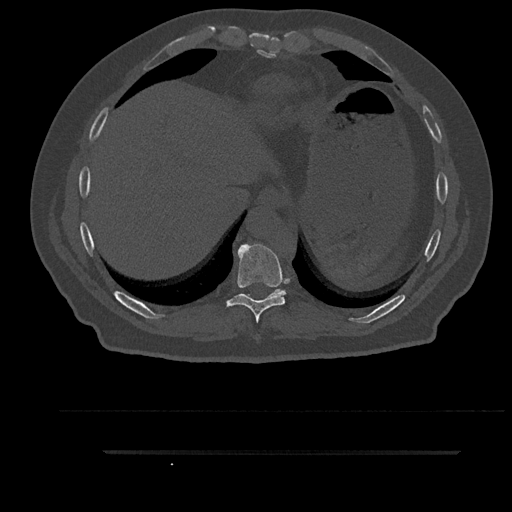
CT including the spine, one axial slice; slice 419 of 797 in the series (ordered by position); reconstruction kernel Br40s/3; 120 kVp; bone window (W 1800 / L 400 HU); 512 × 512 image matrix, field of view 432 × 432 mm. Patient: male, 63 years. Case-level facts recorded for this patient, not image findings: primary cancer: renal; vertebrae with lytic lesions (as recorded): T8.
Outlined on this slice (semi-automatic segmentation, software-assisted and operator-edited):
- T10 vertebra: bounding box (x1, y1, x2, y2) in pixels: (242, 288, 284, 296)
- T9 vertebra: (226, 244, 290, 323)